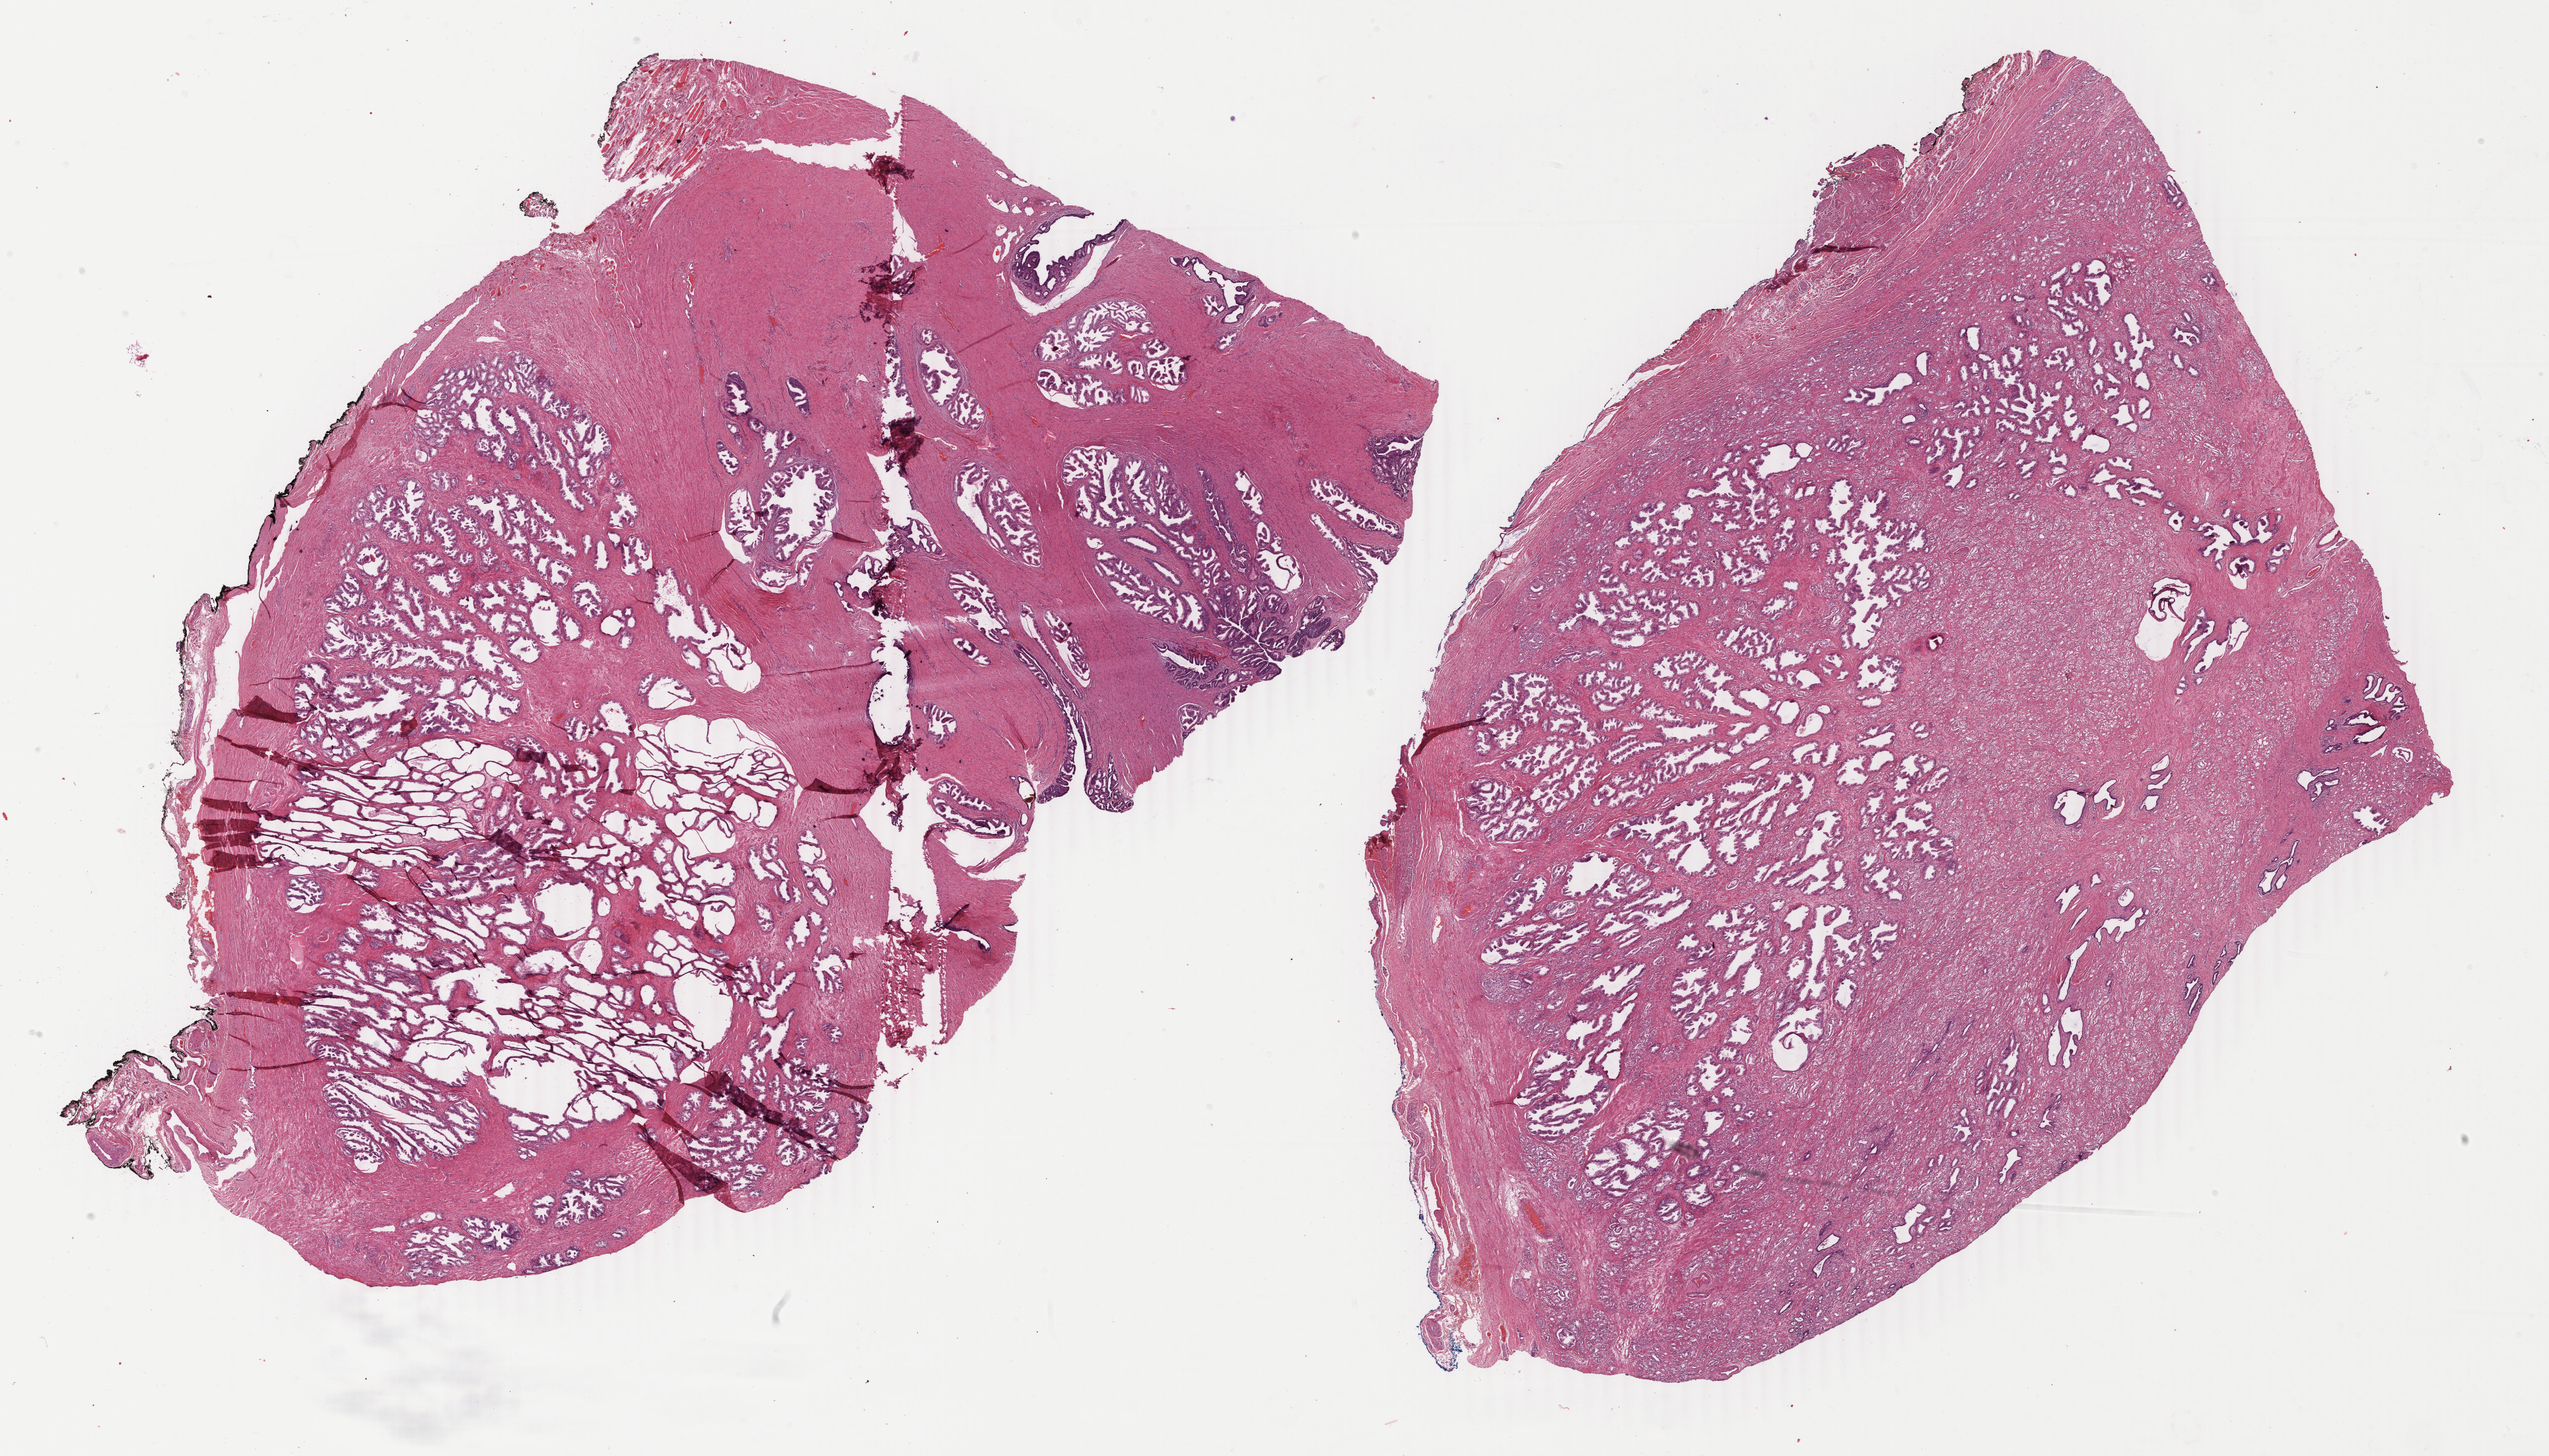
Hematoxylin and eosin (H&E) stained whole-slide image, whole scanned area (about 30.7 x 17.5 mm) shown as a low-resolution overview, formalin-fixed paraffin-embedded (FFPE) diagnostic section, prostate, primary tumour sample. Male patient; age at initial diagnosis 55 years. Gleason score: 7 (4+3).
Pathologic diagnosis: Adenocarcinoma, NOS (prostate gland).